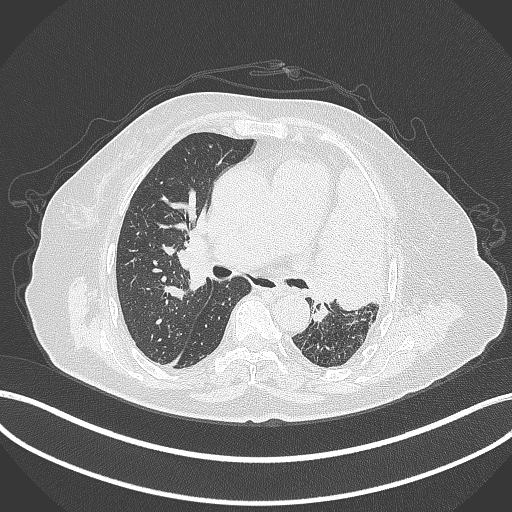
Chest CT, one axial slice. Position 223 of 399 along the scan axis. Lung window (W 1500 / L -600 HU). 512 × 512 image matrix. Female patient, age 75 years. Case-level facts recorded for this patient, not image findings: clinical TNM (as recorded): T3 N3 M1.
Structures marked on this image (rectangle marked by the reading radiologist):
- lung tumour (recorded histology: adenocarcinoma): bounding box (x1, y1, x2, y2) in pixels: (309, 158, 390, 312)